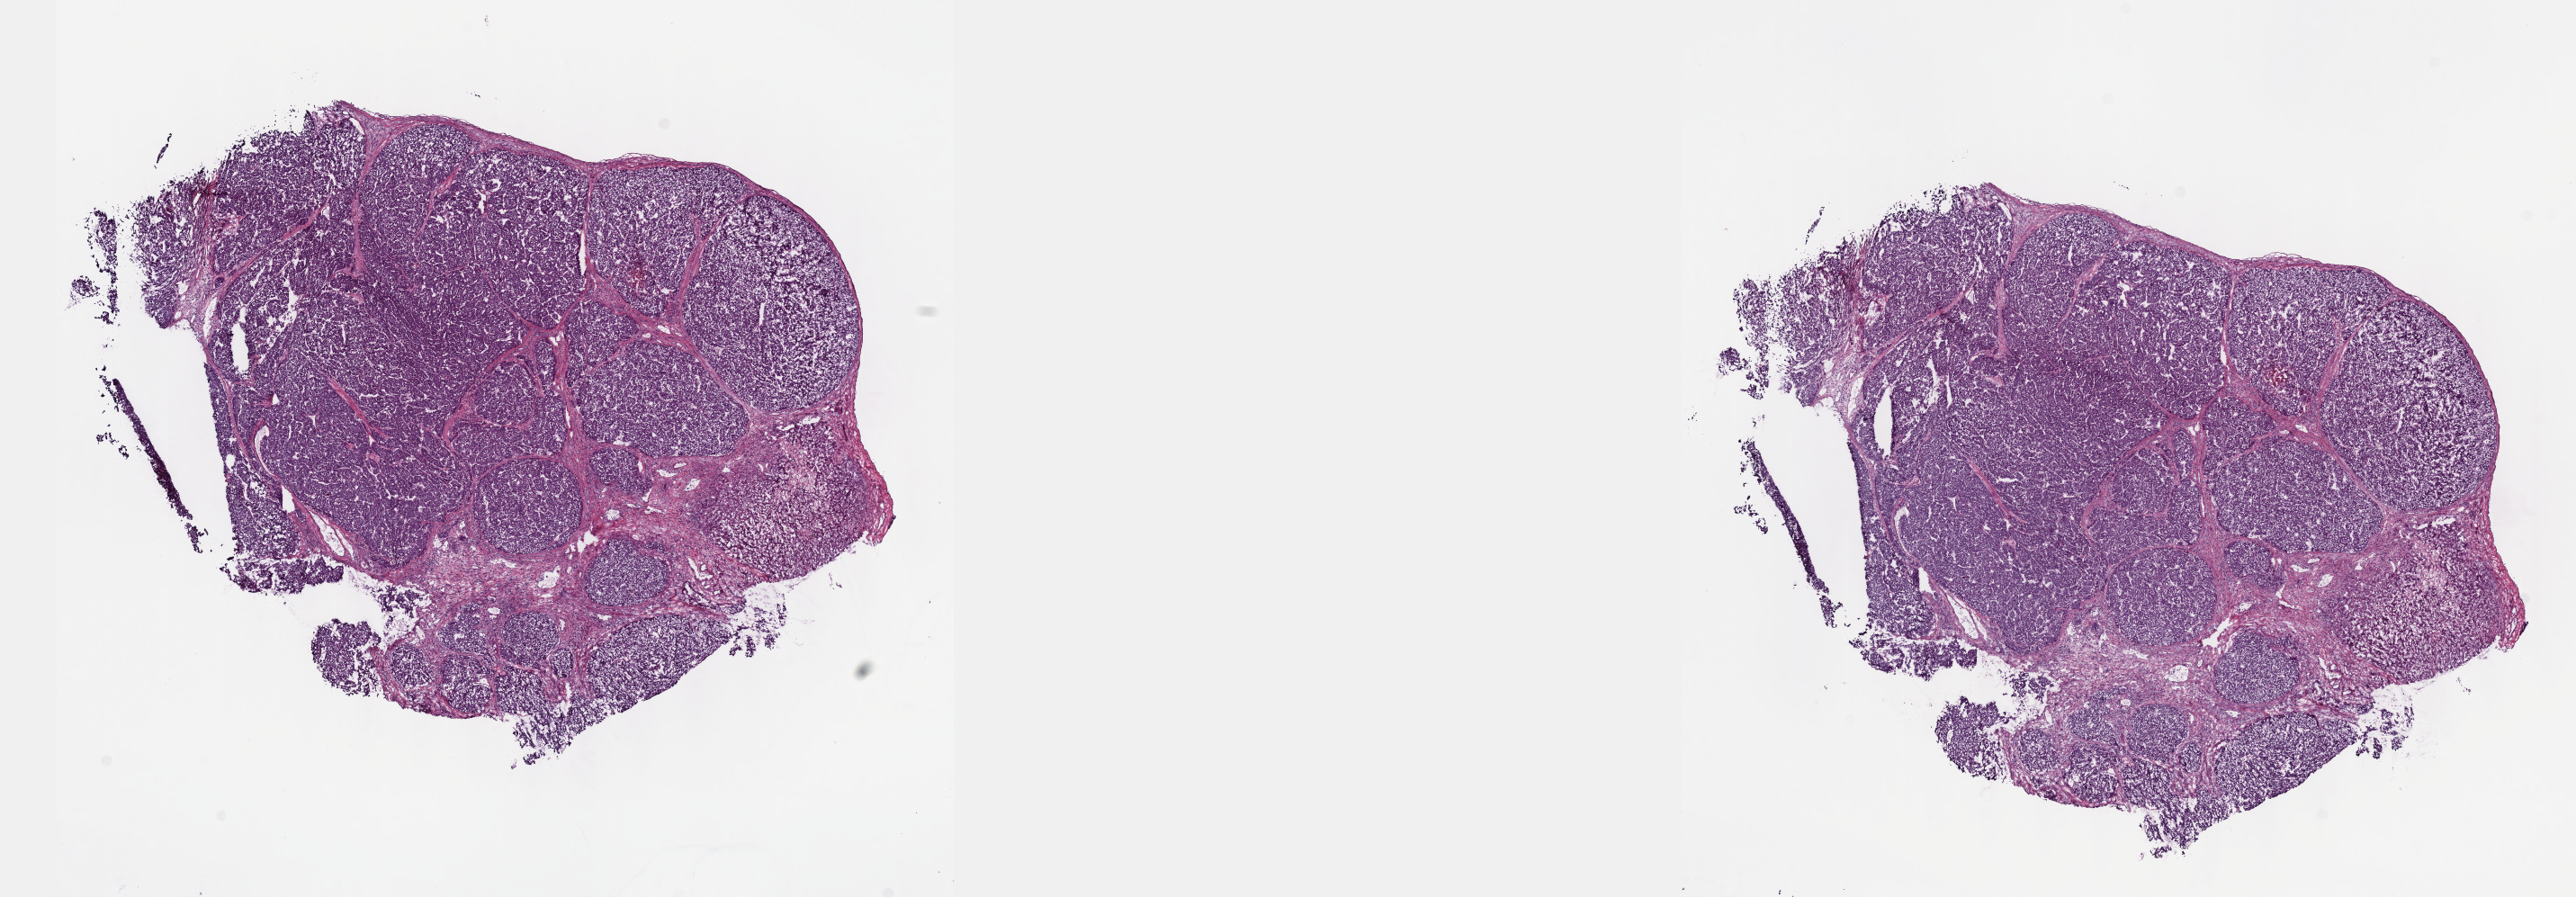
Whole-slide histology image, Hematoxylin and eosin (H&E) stained — a low-resolution overview of the entire scanned area, about 23.1 x 8.1 mm; frozen section from the top of the tissue portion; sample: primary tumour, liver. Patient: male, age at initial diagnosis 69 years. Histologic grade: G3 (poorly differentiated). Slide review estimates, as recorded: tumour cells 80%, tumour nuclei 95%, normal cells 0%, stromal cells 20%, necrosis 0%. Inflammatory infiltration, as recorded: lymphocyte infiltration 0%, monocyte infiltration 0%, neutrophil infiltration 0%.
* AJCC pathologic stage: II (6th edition)
* diagnosis: Hepatocellular carcinoma, NOS